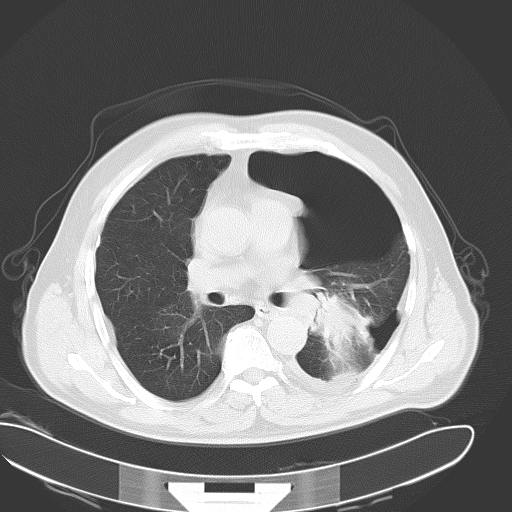
Chest CT, one axial slice; slice 25 of 43 in the series (ordered by position); reconstruction kernel B70f; lung window (W 1500 / L -600 HU); 512 × 512 image matrix, field of view 418 × 418 mm. Male patient, age 62 years. From the clinical record (not read from this slice): clinical TNM (as recorded): T3 N0 M1.
Structures marked on this image (bounding box drawn by a radiologist):
- lung tumour (recorded histology: adenocarcinoma): bounding box [x1, y1, x2, y2] px = [301, 283, 374, 358]
- lung tumour (recorded histology: adenocarcinoma): [319, 282, 373, 348]